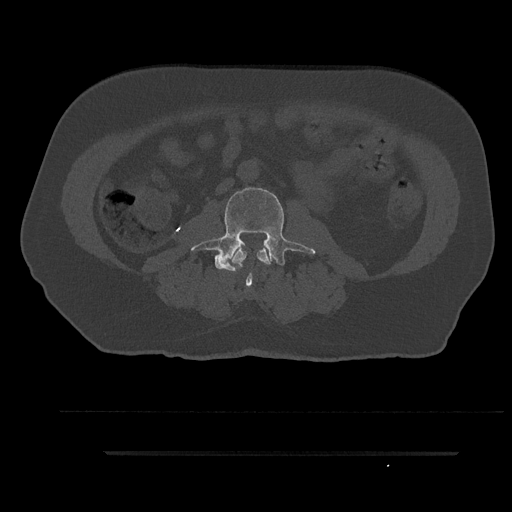
CT including the spine, one axial slice. Slice 57 of 797 in the series (ordered by position). Reconstruction kernel Br40s/3. 120 kVp. Bone window (W 1800 / L 400 HU). 0.5 mm slice thickness. 512 × 512 image matrix, field of view 432 × 432 mm. Male patient, age 63 years. From the clinical record (not read from this slice): primary cancer: renal; vertebrae with lytic lesions (as recorded): T8.
Outlined on this slice (semi-automatically segmented with operator editing):
- L2 vertebra: bounding box [x1, y1, x2, y2] px = [232, 248, 270, 272]
- L3 vertebra: [190, 185, 315, 286]